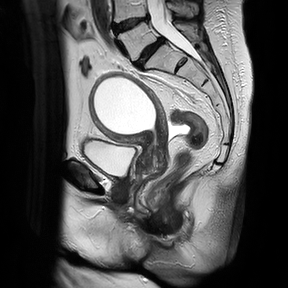
Pelvic MRI for cervical cancer, one sagittal slice. Position 16 of 30 along the scan axis. T2-weighted. 1.5 T. TE 100 ms, TR 4816.3 ms. 4 mm slice thickness. 288 × 288 image matrix, field of view 300 × 300 mm. Patient: female, 74 years.
Structures marked on this image (expert manual segmentation):
- uterus and cervix: box from (x=88, y=71) to (x=169, y=186) px